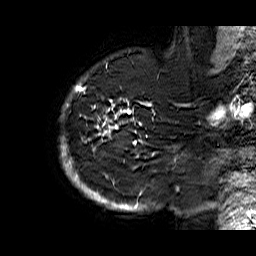
Breast MRI (dynamic contrast-enhanced), one sagittal slice; dynamic contrast-enhanced series, time point 2 of 6 at this slice position (early post-contrast); 1.5 T; TE 6.3 ms, TR 32.9 ms; 4 mm slice thickness; 256 × 256 image matrix. Female patient. Case-level facts recorded for this patient, not image findings: setting: breast cancer imaged before/during neoadjuvant chemotherapy; receptor status: HR-positive, HER2-negative.
Outlined on this slice (semi-automatic segmentation, software-assisted and operator-edited):
- analysis volume of interest (the breast-tissue region the enhancement analysis was run in; not a lesion): box from (x=59, y=74) to (x=176, y=210) px
- tumour enhancement mask (voxels above the 100 % enhancement threshold inside the analysis volume of interest): (x=60, y=77)–(x=175, y=210)